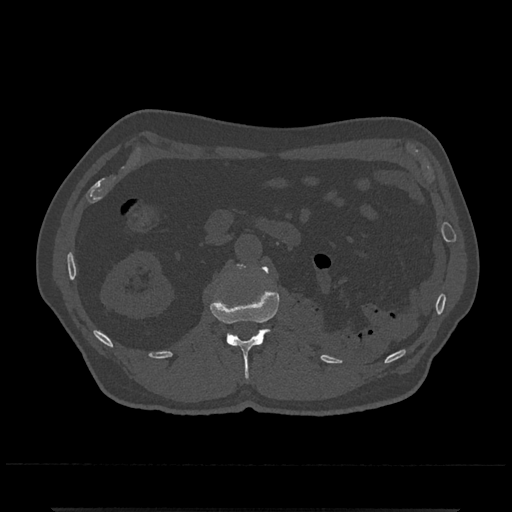
CT including the spine, one axial slice; slice 346 of 797 in the series (ordered by position); reconstruction kernel Br40s/3; 120 kVp; bone window (W 1800 / L 400 HU); 0.5 mm slice thickness; 512 × 512 image matrix. Male patient, age 67 years. From the clinical record (not read from this slice): primary cancer: prostate.
Structures marked on this image (semi-automatic segmentation, software-assisted and operator-edited):
- L1 vertebra: bounding box (x1, y1, x2, y2) in pixels: (210, 266, 280, 379)
- L2 vertebra: (237, 264, 245, 268)